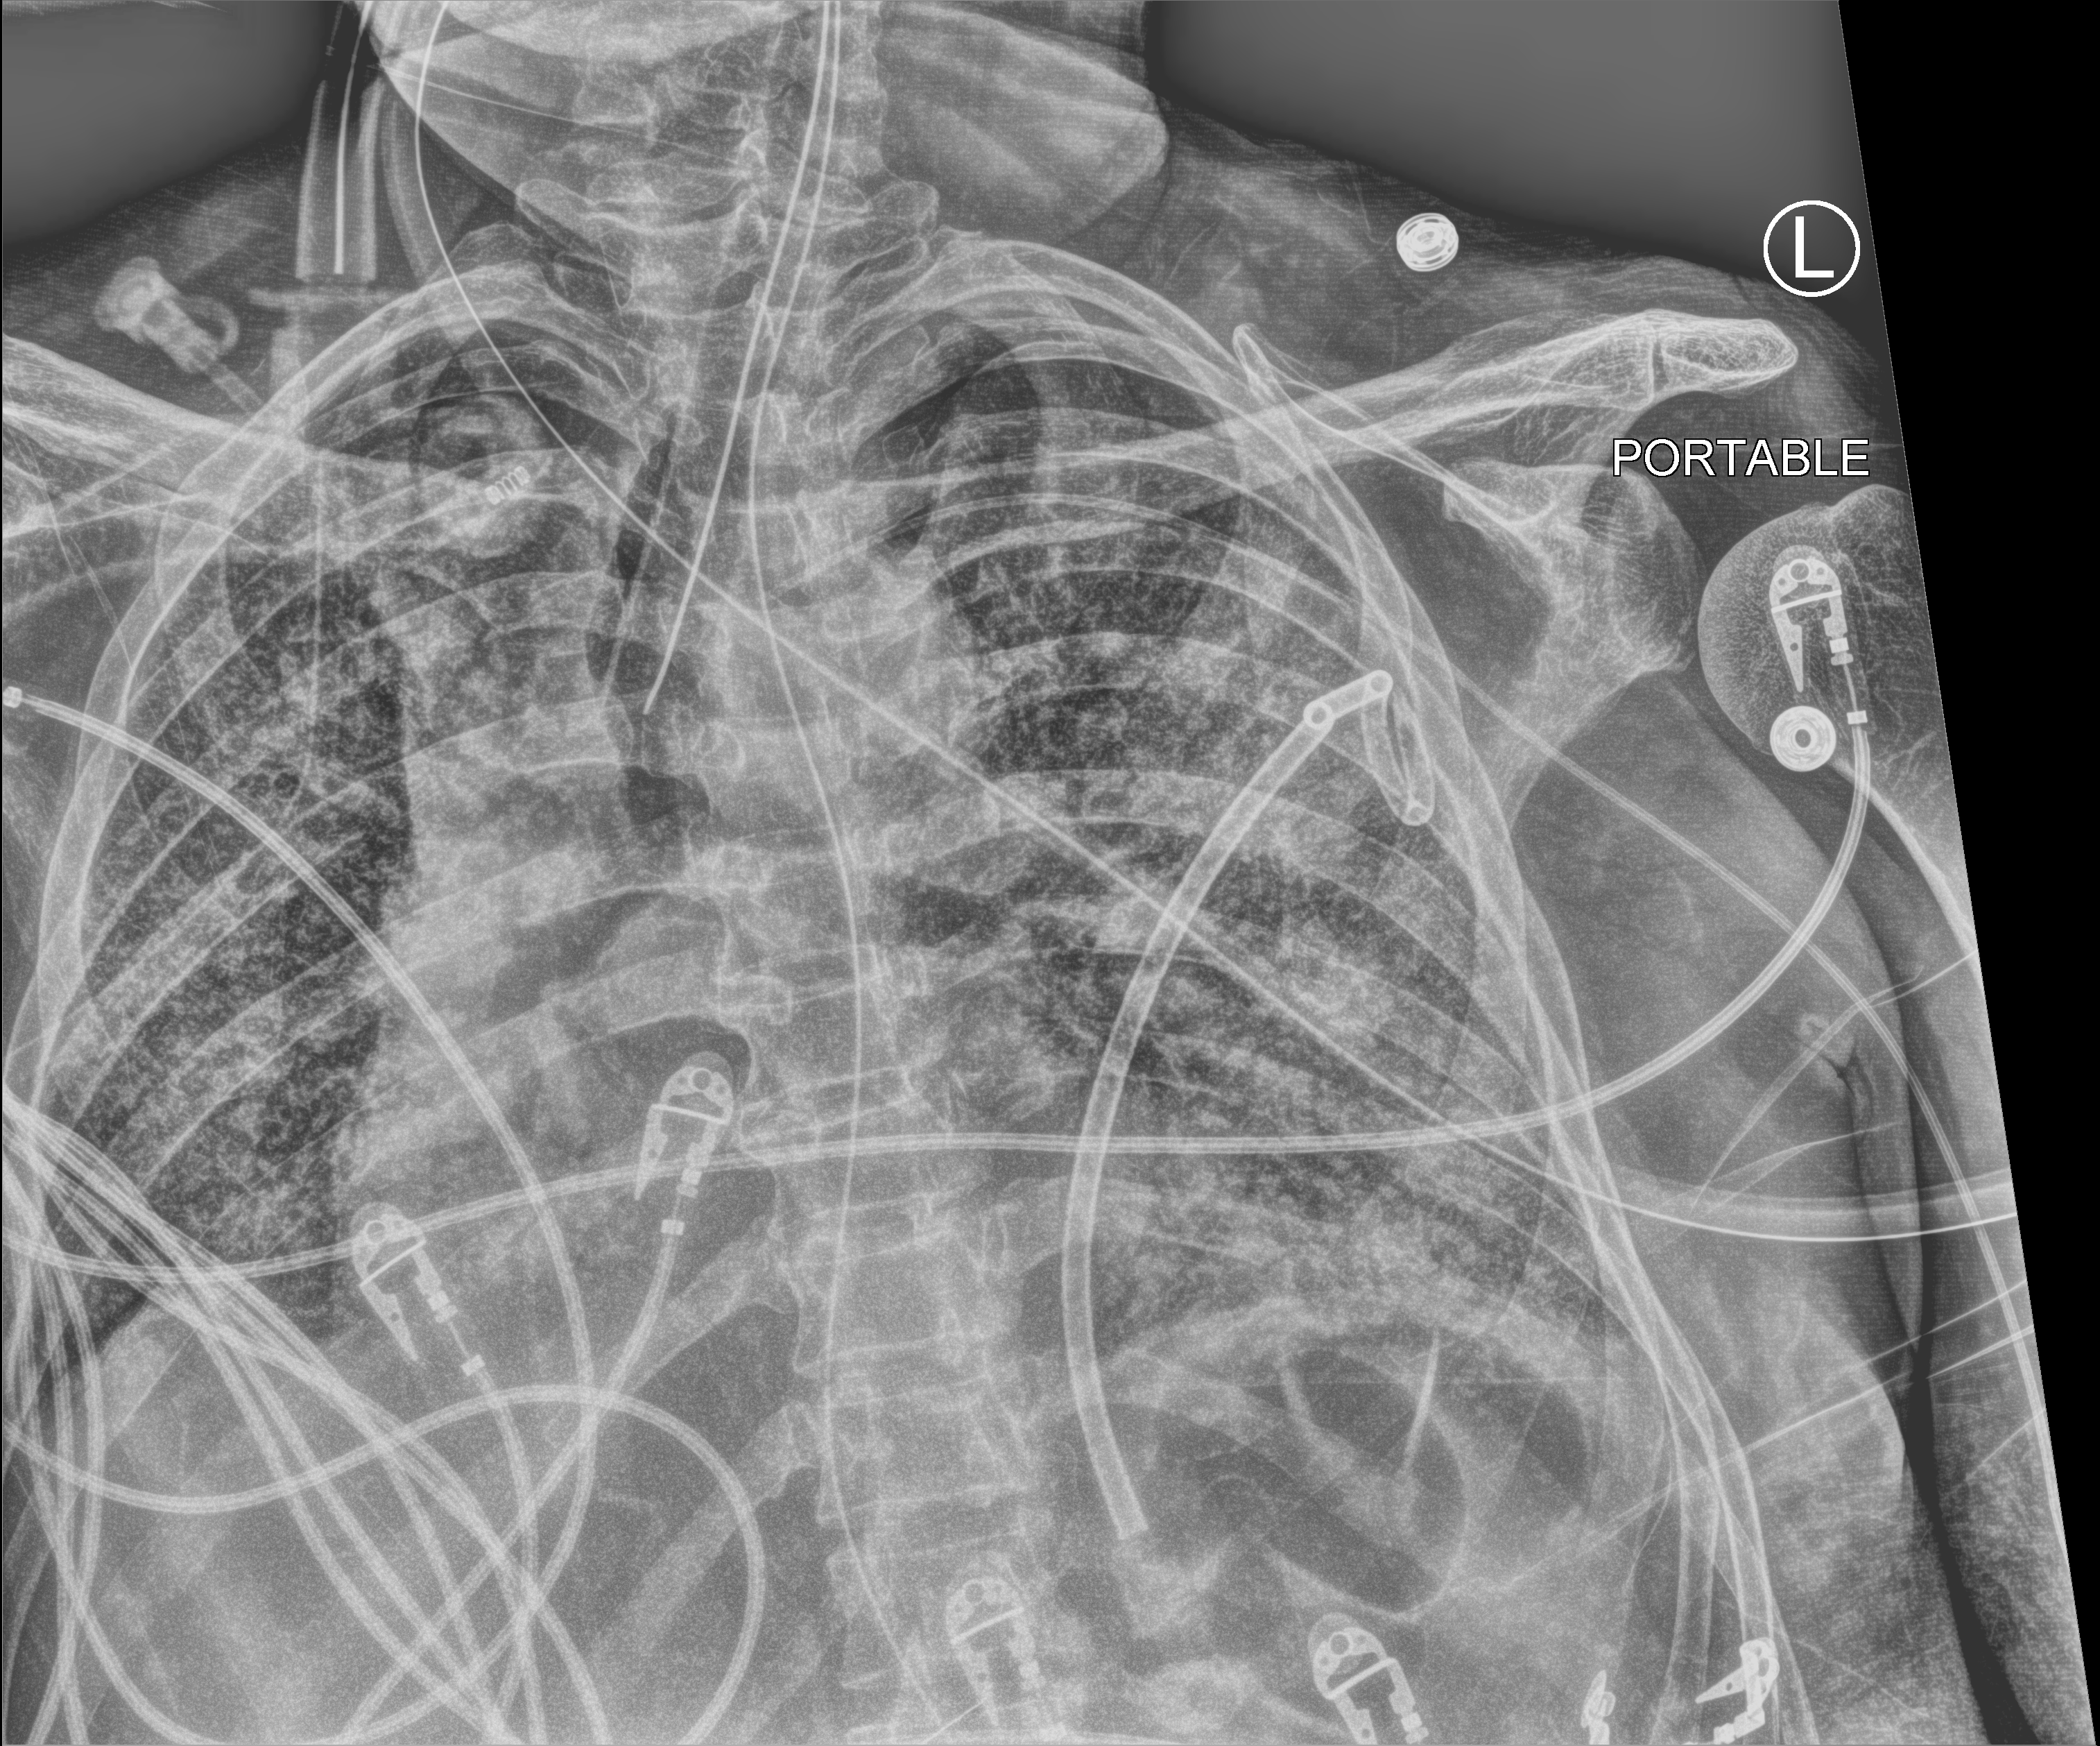
Portable chest radiograph, anteroposterior (AP) projection. Patient hospitalised with COVID-19; male, aged 60–74 years.
From the hospital-stay record, not from the radiograph (when in the stay this image was taken is not recorded):
- admitted to intensive care during this hospital stay: yes